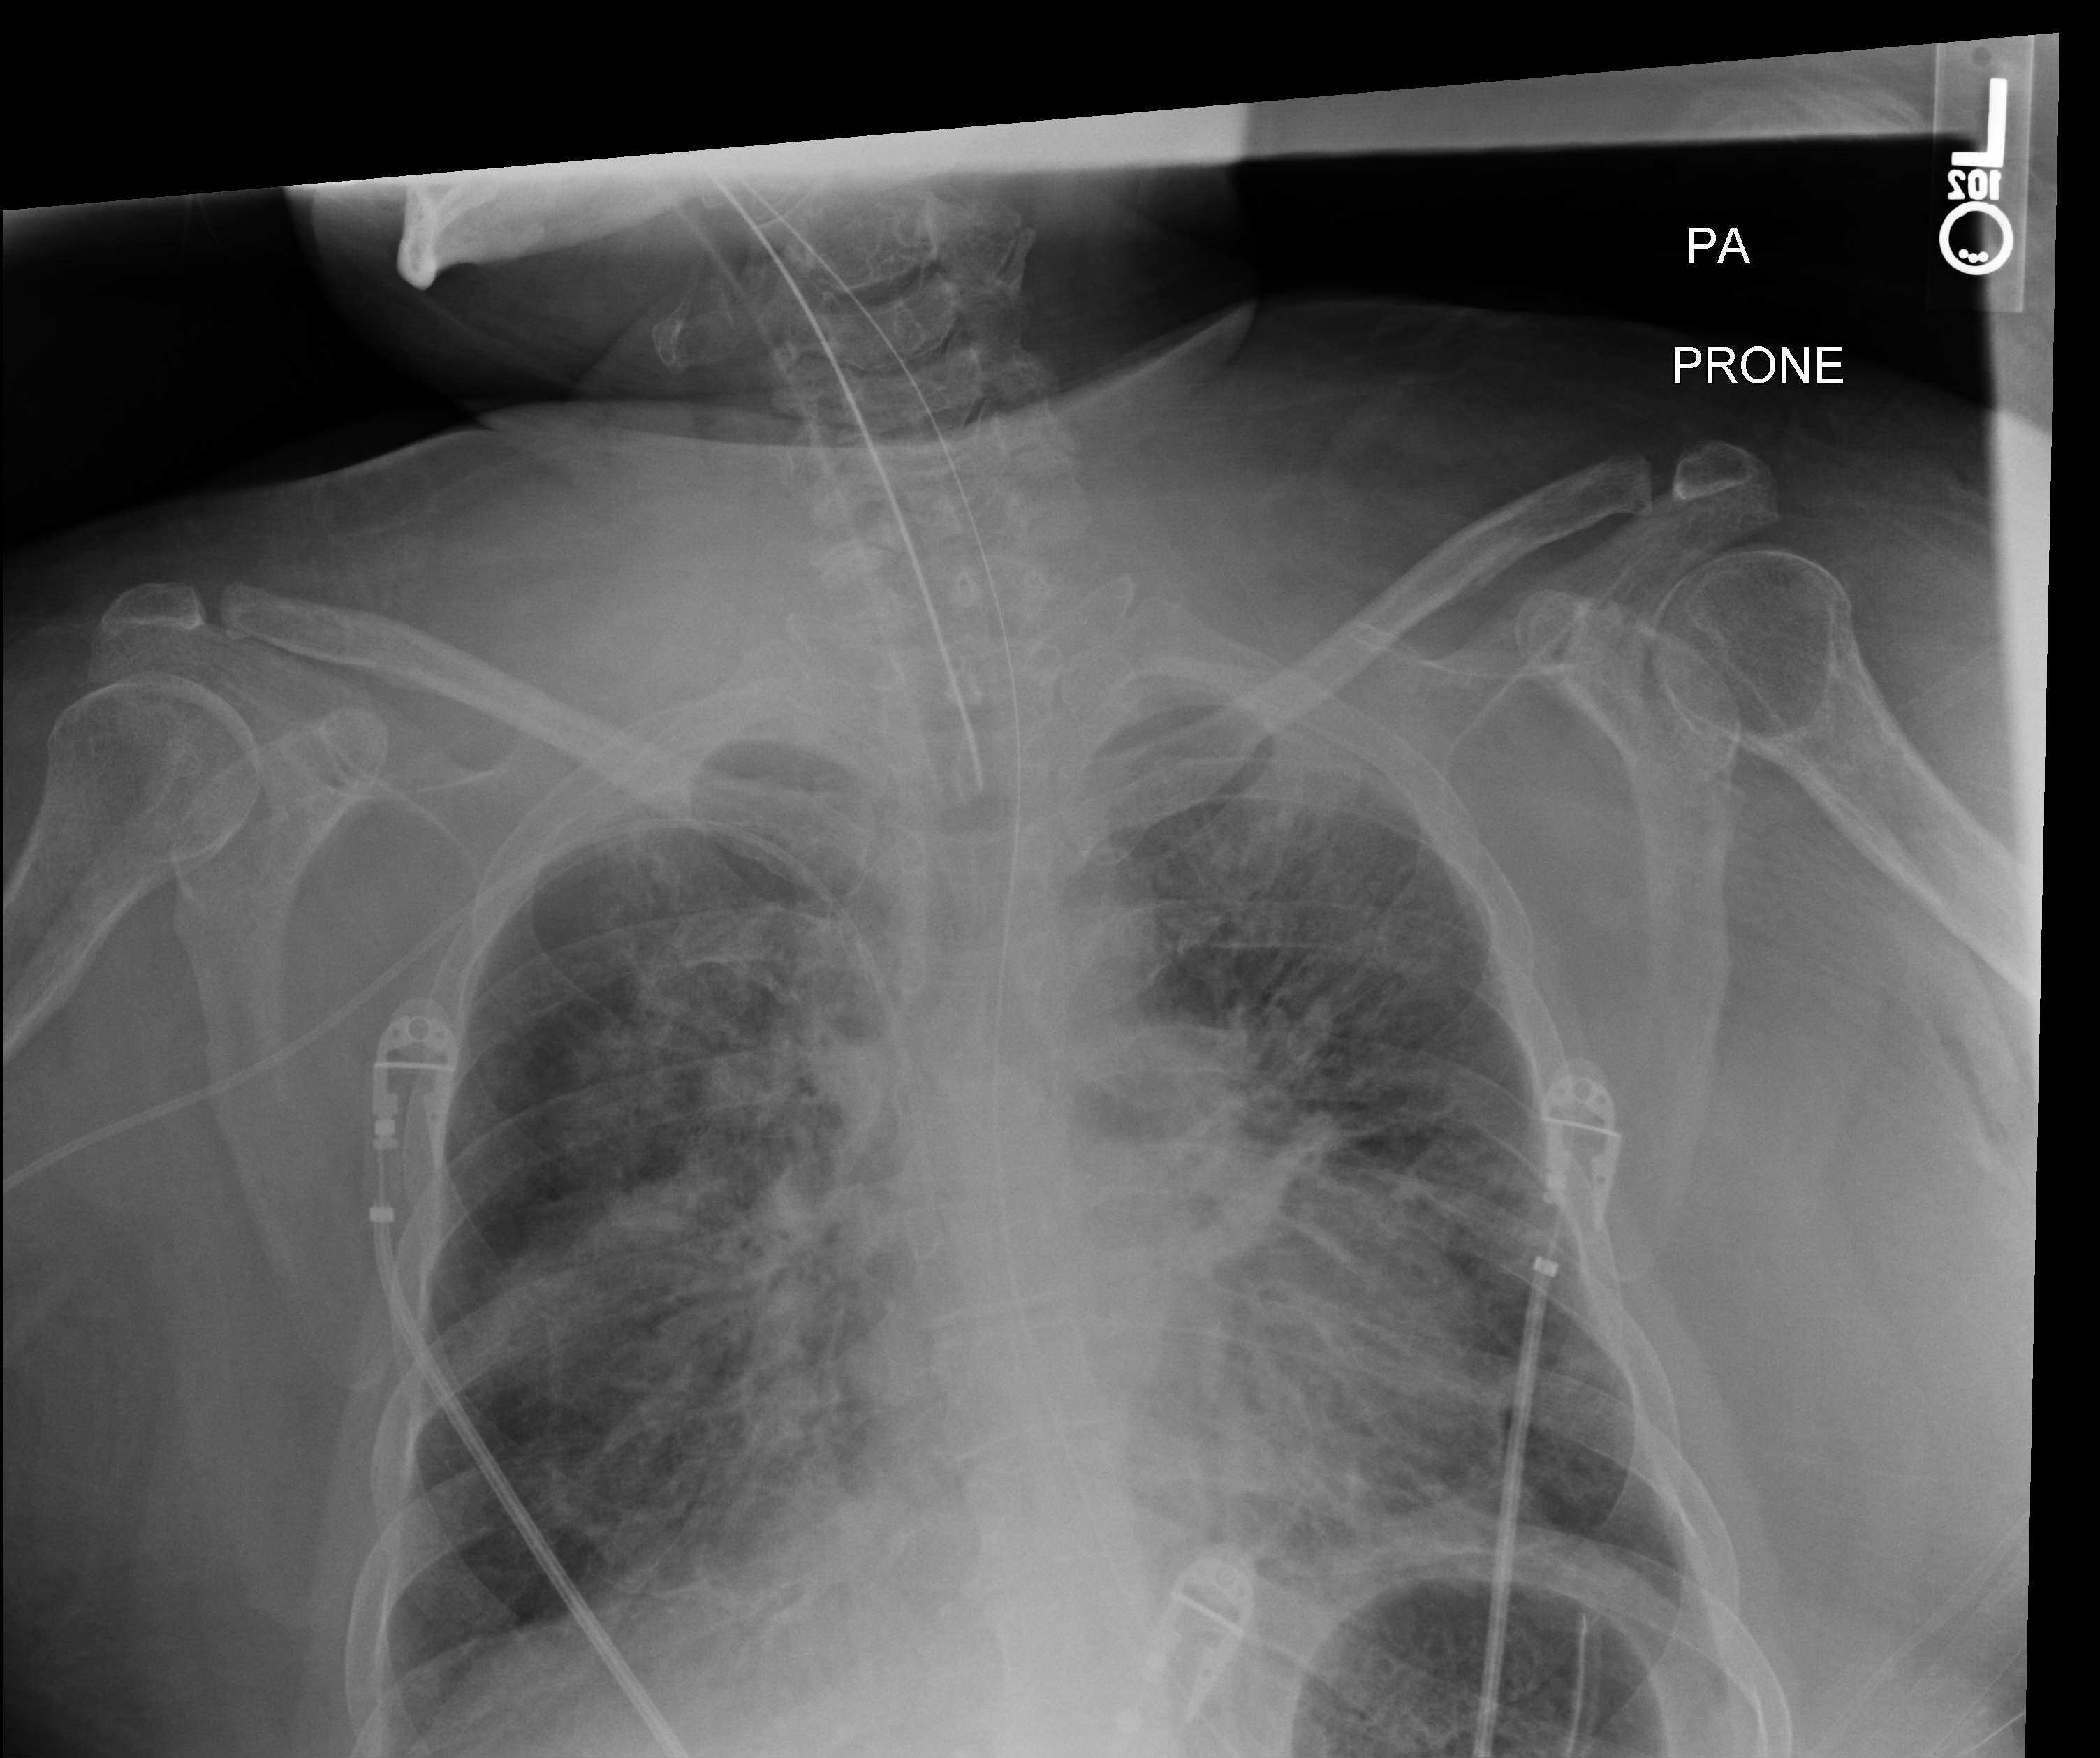
Chest X-ray (portable), posteroanterior (PA) projection. Patient hospitalised with COVID-19, aged 18–59 years.
From the hospital-stay record, not from the radiograph (when in the stay this image was taken is not recorded): admitted to intensive care during this hospital stay: yes; length of hospital stay: 15 days.